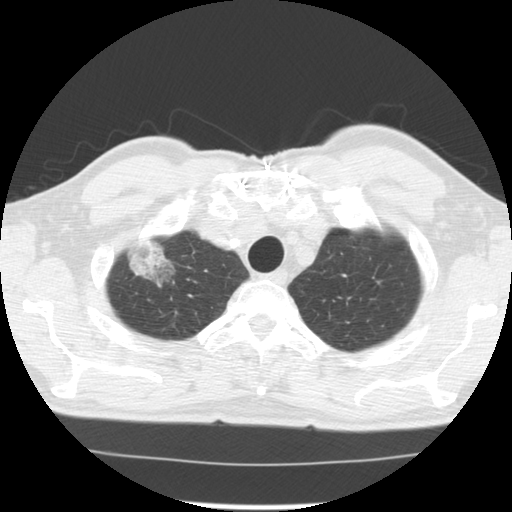
Low-dose screening chest CT, axial slice; third screening round (two years after baseline); lung window (W 1500 / L -600 HU); 2.5 mm slice thickness; standard (soft-tissue) reconstruction kernel (STANDARD). Male, age 64 years at enrolment. Former smoker at enrolment.
Expert-annotated lung lesion, bounding box <120,235,190,294> (left, top, right, bottom; pixels). The screening reader recorded 3 non-calcified nodules or masses ≥4 mm on this exam (right upper lobe, right lower lobe, left upper lobe); which of them this box marks is not recorded. Official screen result: positive, other. Participant outcome: lung cancer diagnosed 30 days after this screen — adenocarcinoma, NOS, right upper lobe, well differentiated (G1), stage IB (AJCC 6th edition), 45 mm at pathology.